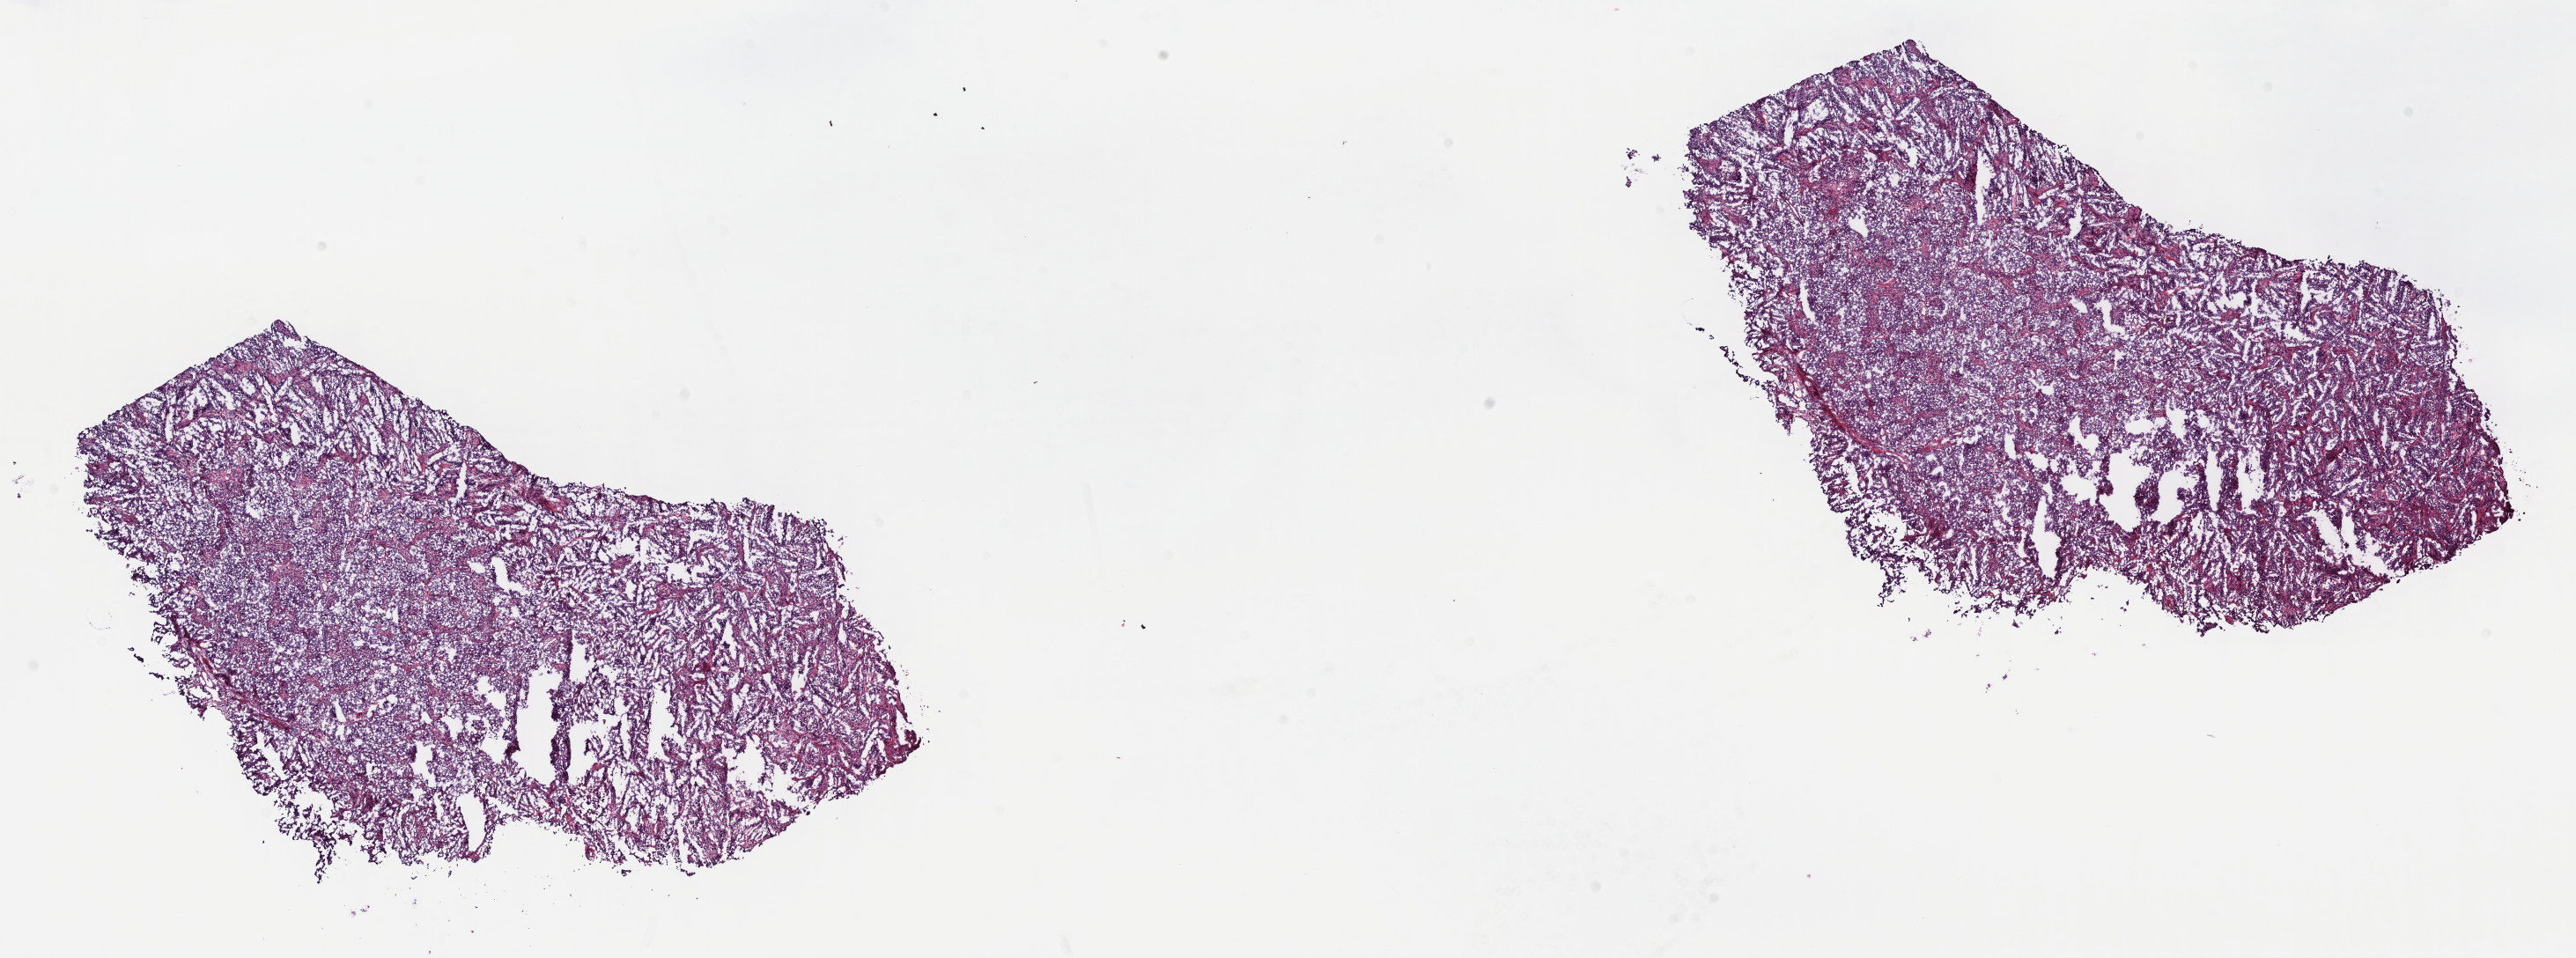
Digitized H&E tissue section (whole slide) — whole scanned area (about 23.7 x 8.8 mm, slide scanned at 40x) shown as a low-resolution overview; frozen section from the top of the tissue portion; testis, primary tumour sample. Male, age 48 years at initial diagnosis. Pathologist review of this section (percent, as recorded): tumour cells 100%, tumour nuclei 65%, normal cells 0%, stromal cells 0%, necrosis 0%. Infiltration values recorded for this section: lymphocyte infiltration 2%, monocyte infiltration 0%, neutrophil infiltration 0%.
Laterality: left. Histologic diagnosis: Seminoma, NOS. AJCC pathologic stage: IB (6th edition).